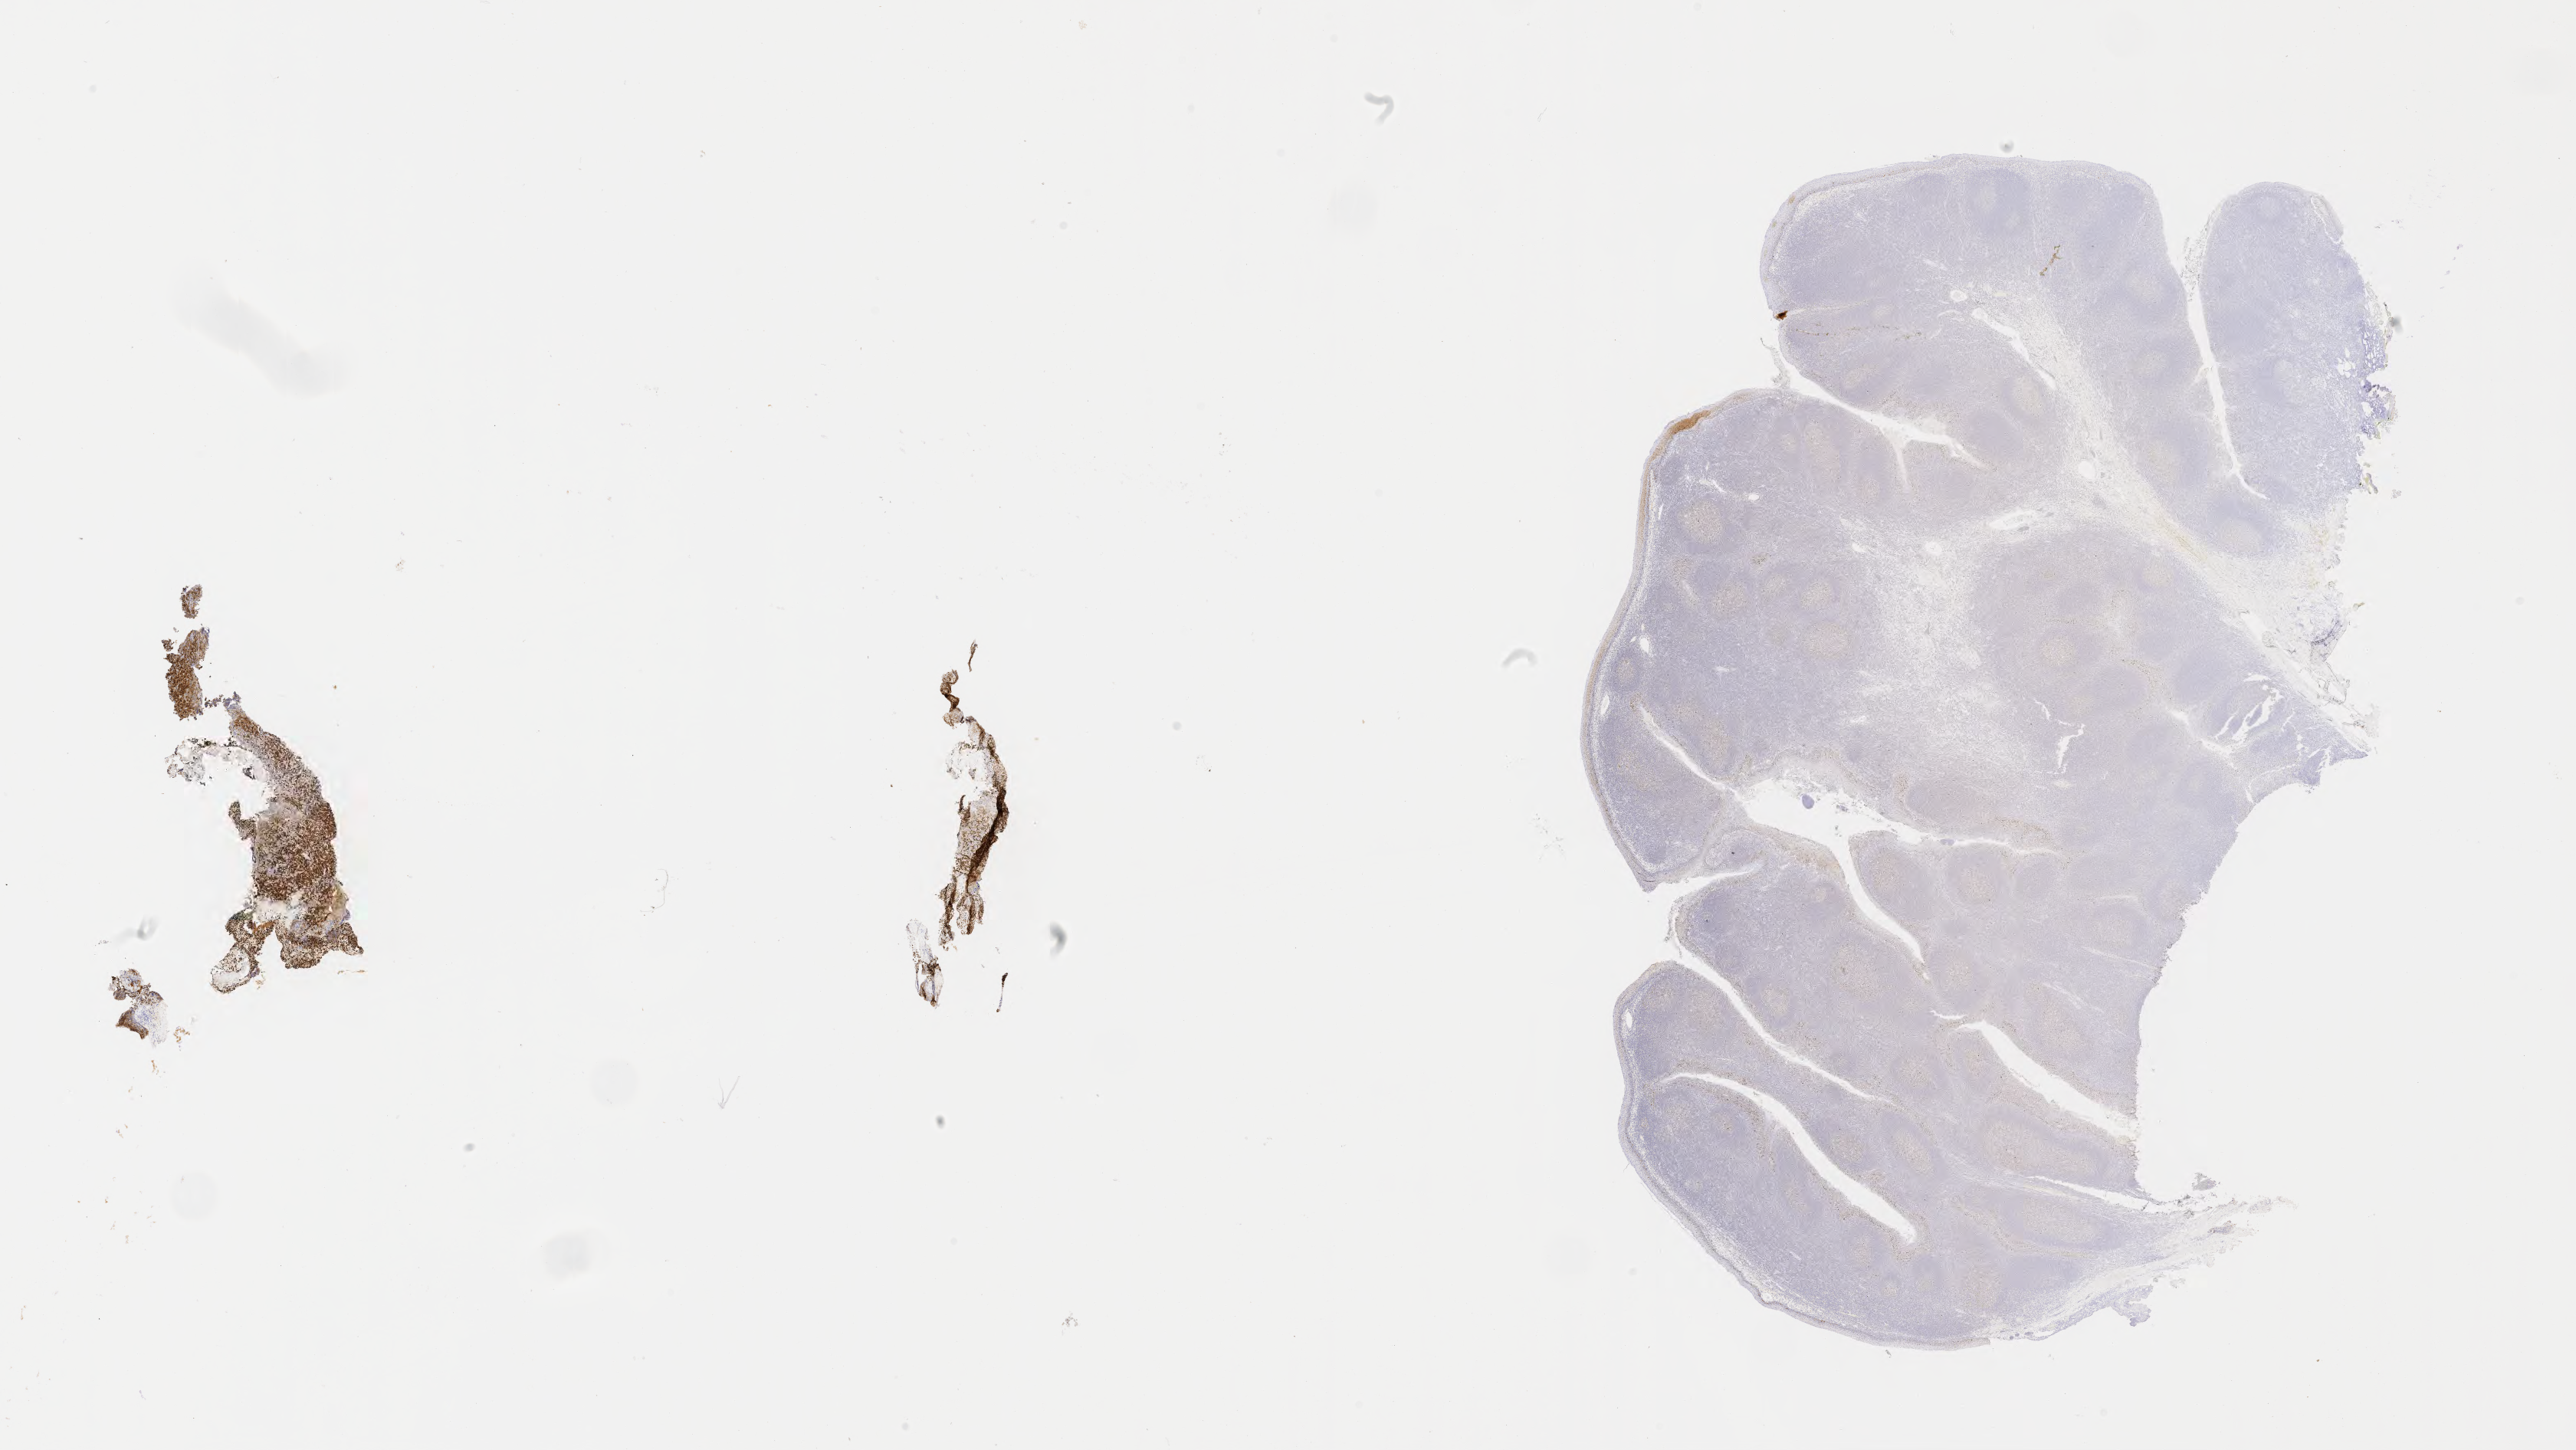
IHC for p53, whole-slide image — shown as a low-resolution overview of the whole scanned area (about 27.2 x 15.3 mm); specimen: tumor tissue. Patient: female, aged 27.
Diagnosis: Diffuse large B-cell lymphoma, NOS.